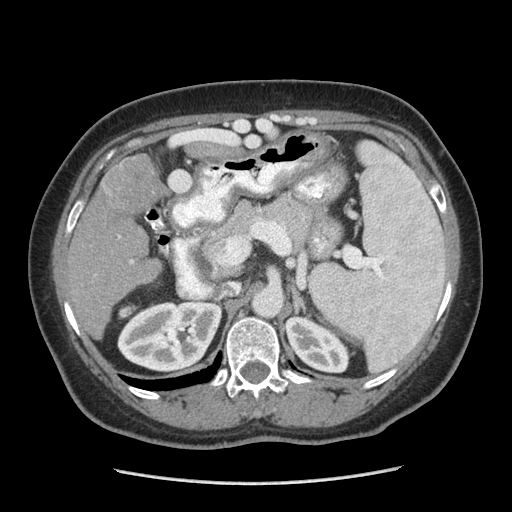
Contrast-enhanced abdominal CT (liver protocol), one axial slice; position 145 of 185 along the scan axis; reconstruction kernel STANDARD; 140 kVp; soft-tissue window (W 400 / L 40 HU); 512 × 512 image matrix, field of view 360 × 360 mm. Case-level facts recorded for this patient, not image findings: diagnosis: hepatocellular carcinoma (patient treated with transarterial chemoembolisation; whether this scan precedes or follows treatment is not stated here); TNM stage (as recorded): Stage-I; Child-Pugh class: A; tumour differentiation: poorly differentiated.
Annotated regions visible in this slice (semi-automatically segmented with operator editing):
- liver parenchyma outside the tumour (the mass and vessels are separate outlines, so this box may not span the whole liver): bounding box (x1, y1, x2, y2) in pixels: (64, 154, 162, 336)
- mass: (98, 157, 162, 214)
- liver vessels: (119, 236, 133, 264)